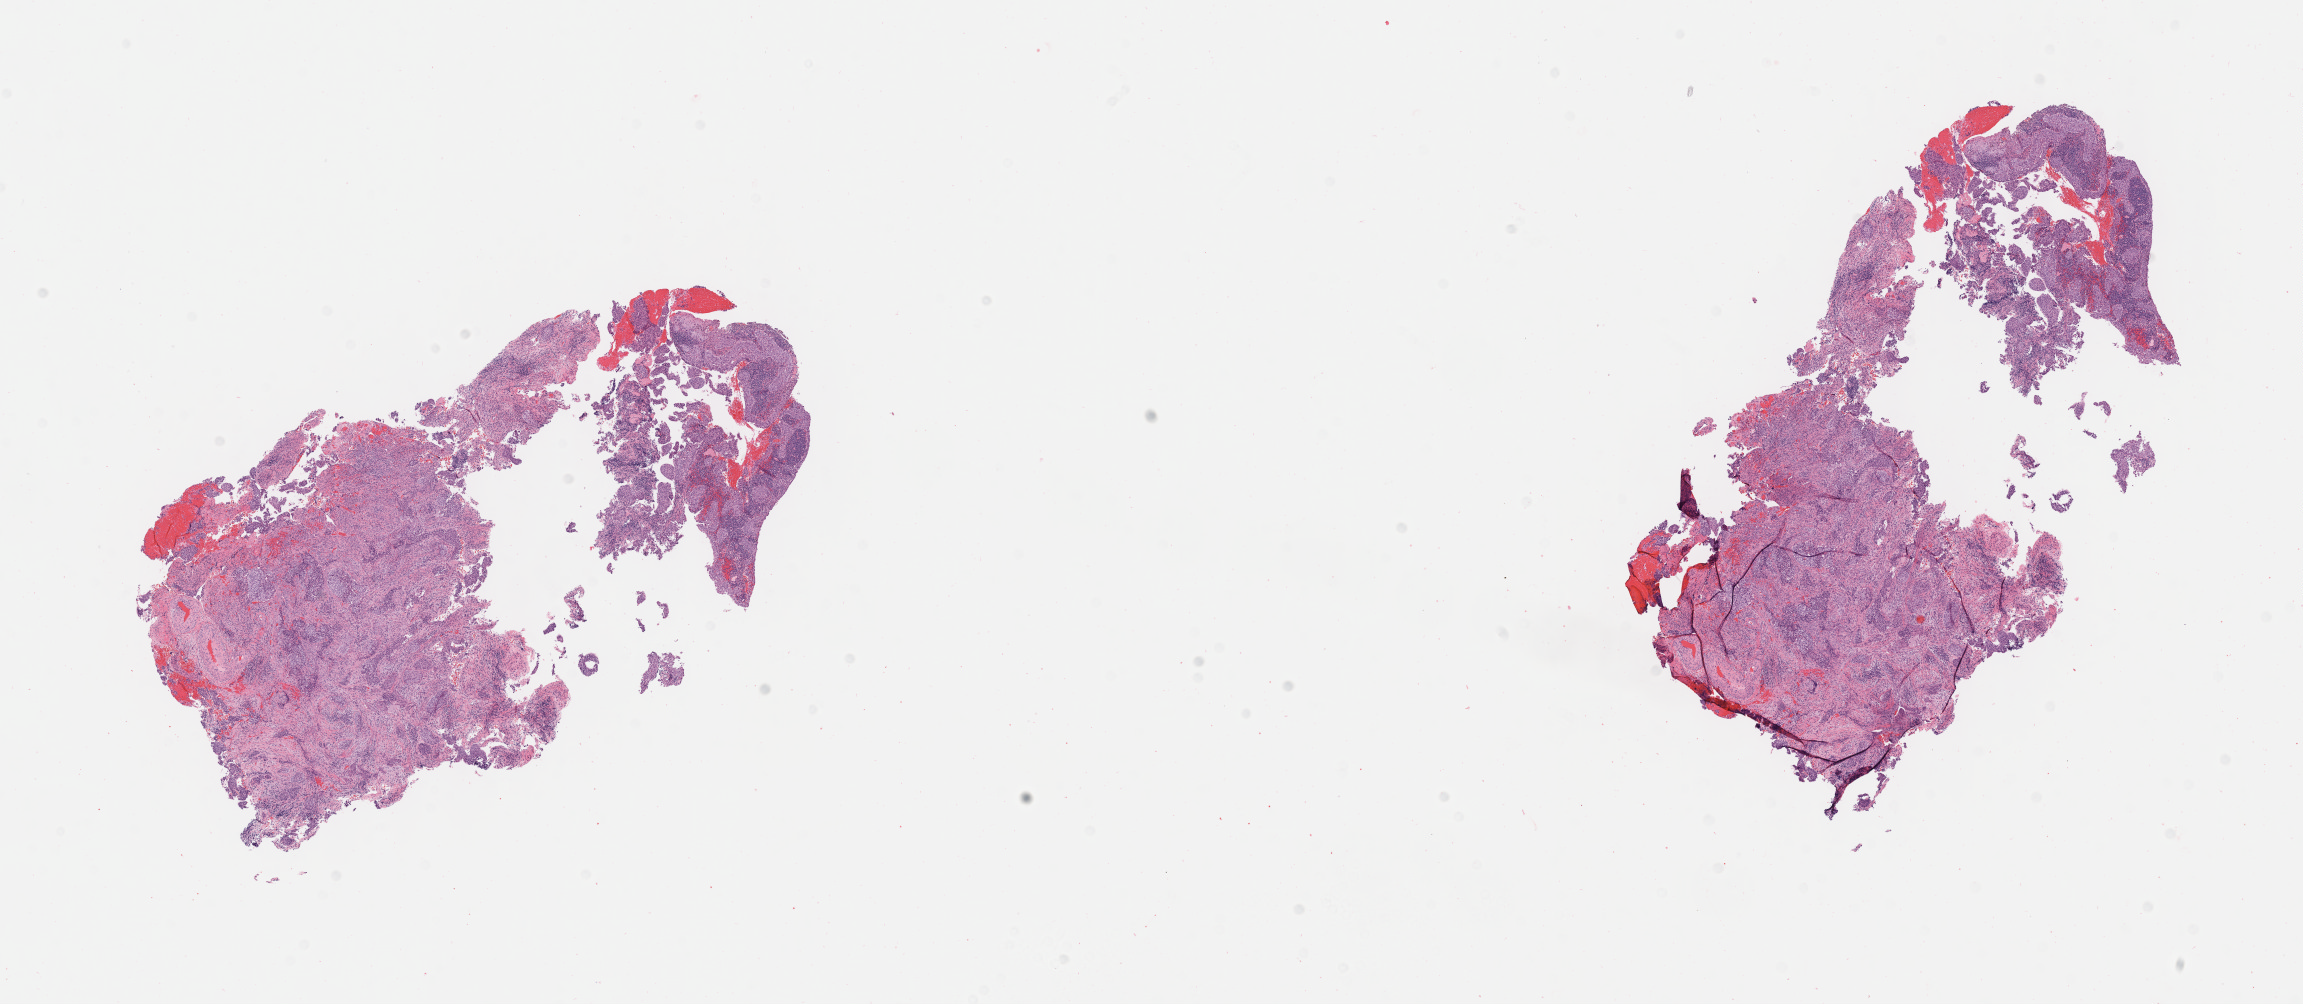
H&E whole-slide image, whole scanned area (about 18.6 x 8.1 mm) shown as a low-resolution overview, specimen: tumor tissue, site: cervix. Female patient, 28 years old.
Histologic diagnosis: Squamous cell carcinoma, large cell, nonkeratinizing, NOS.